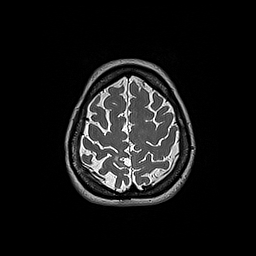
Brain MRI from a brain-tumour surgery series, one axial slice. Position 48 of 192 along the scan axis. 1 mm slice thickness. 256 × 256 image matrix, field of view 250 × 250 mm. Case-level facts recorded for this patient, not image findings: histopathology: Oligodendroglioma; WHO grade: 2.
Annotated regions visible in this slice (expert manual segmentation):
- tumour: bounding box [x1, y1, x2, y2] px = [115, 156, 118, 161]